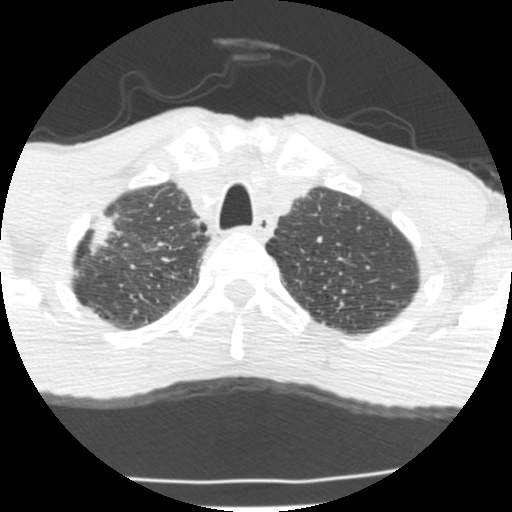
Low-dose screening chest CT, one axial slice; position 183 of 214 along the scan axis; 120 kVp; lung window (W 1500 / L -600 HU); 2.5 mm slice thickness; 512 × 512 image matrix, field of view 283 × 283 mm.
Structures marked on this image (expert manual segmentation):
- lesion 1 (tumor, upper lobe of right lung): box from (x=89, y=214) to (x=118, y=256) px